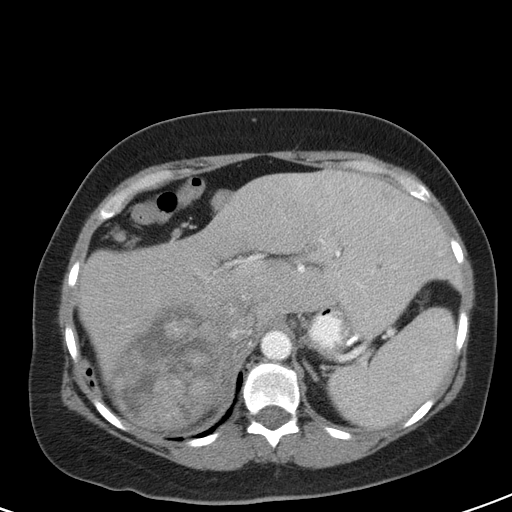
Contrast-enhanced abdominal CT, one axial slice; slice 77 of 126 in the series (ordered by position); intravenous contrast given; soft-tissue window (W 400 / L 40 HU); 5 mm slice thickness; 512 × 512 image matrix, field of view 356 × 356 mm. Female patient, age 51 years. From the clinical record (not read from this slice): diagnosis: adrenocortical carcinoma; tumour side: right adrenal; tumour size at pathology: 17 cm; Ki-67 index: 12 %; stage (as recorded): 2.
Annotated regions visible in this slice (semi-automatic segmentation, software-assisted and operator-edited):
- mass: bounding box <114,300,250,429> (left, top, right, bottom; pixels)